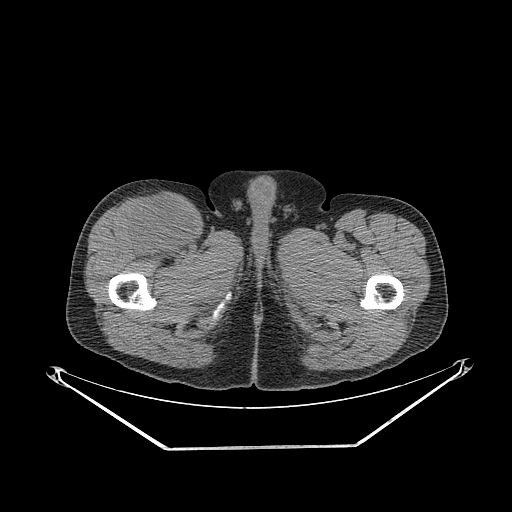
CT of an extremity soft-tissue mass (from a PET/CT study), one axial slice. Slice 300 of 311 in the series (ordered by position). Reconstruction kernel STANDARD. 140 kVp. Soft-tissue window (W 400 / L 40 HU). 3.75 mm slice thickness. 512 × 512 image matrix, field of view 500 × 500 mm. Male patient. From the clinical record (not read from this slice): histological type: pleiomorphic leiomyosarcoma; grade: intermediate; site of the primary tumour: right thigh.
Structures marked on this image (expert contour drawn on MRI and transferred to this co-registered scan by the dataset authors):
- gross tumour volume including surrounding oedema: bounding box [x1, y1, x2, y2] px = [128, 196, 197, 255]
- gross tumour volume (mass): [130, 201, 197, 254]